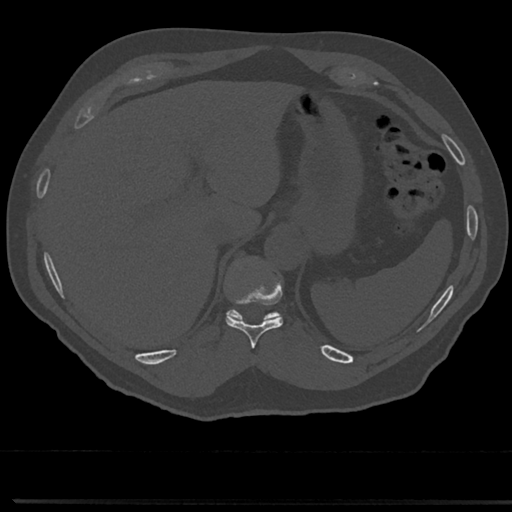
CT including the spine, one axial slice; slice 242 of 817 in the series (ordered by position); reconstruction kernel Br40s/3; 120 kVp; bone window (W 1800 / L 400 HU); 512 × 512 image matrix. Male patient, age 61 years. Case-level facts recorded for this patient, not image findings: primary cancer: prostate.
Outlined on this slice (semi-automatic segmentation, software-assisted and operator-edited):
- T10 vertebra: bounding box [x1, y1, x2, y2] px = [226, 257, 284, 346]
- T11 vertebra: [228, 312, 278, 321]